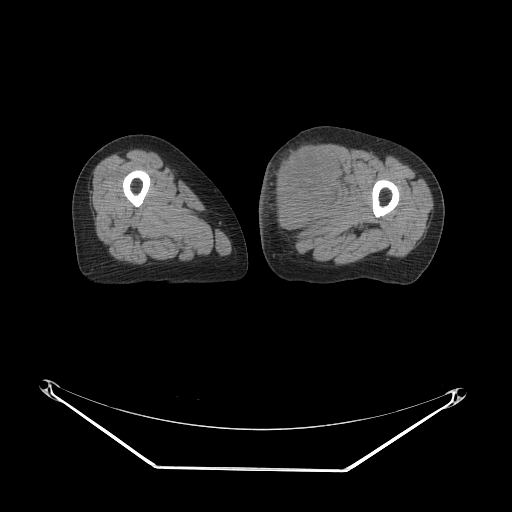
CT of an extremity soft-tissue mass (from a PET/CT study), one axial slice; position 39 of 91 along the scan axis; reconstruction kernel STANDARD; 140 kVp; soft-tissue window (W 400 / L 40 HU); 512 × 512 image matrix. Female patient. From the clinical record (not read from this slice): histological type: pleomorphic leiomyosarcoma; grade: high; site of the primary tumour: left thigh.
Structures marked on this image (expert contour drawn on MRI and transferred to this co-registered scan by the dataset authors):
- gross tumour volume including surrounding oedema: bounding box [x1, y1, x2, y2] px = [269, 142, 346, 238]
- gross tumour volume (mass): [272, 142, 344, 229]